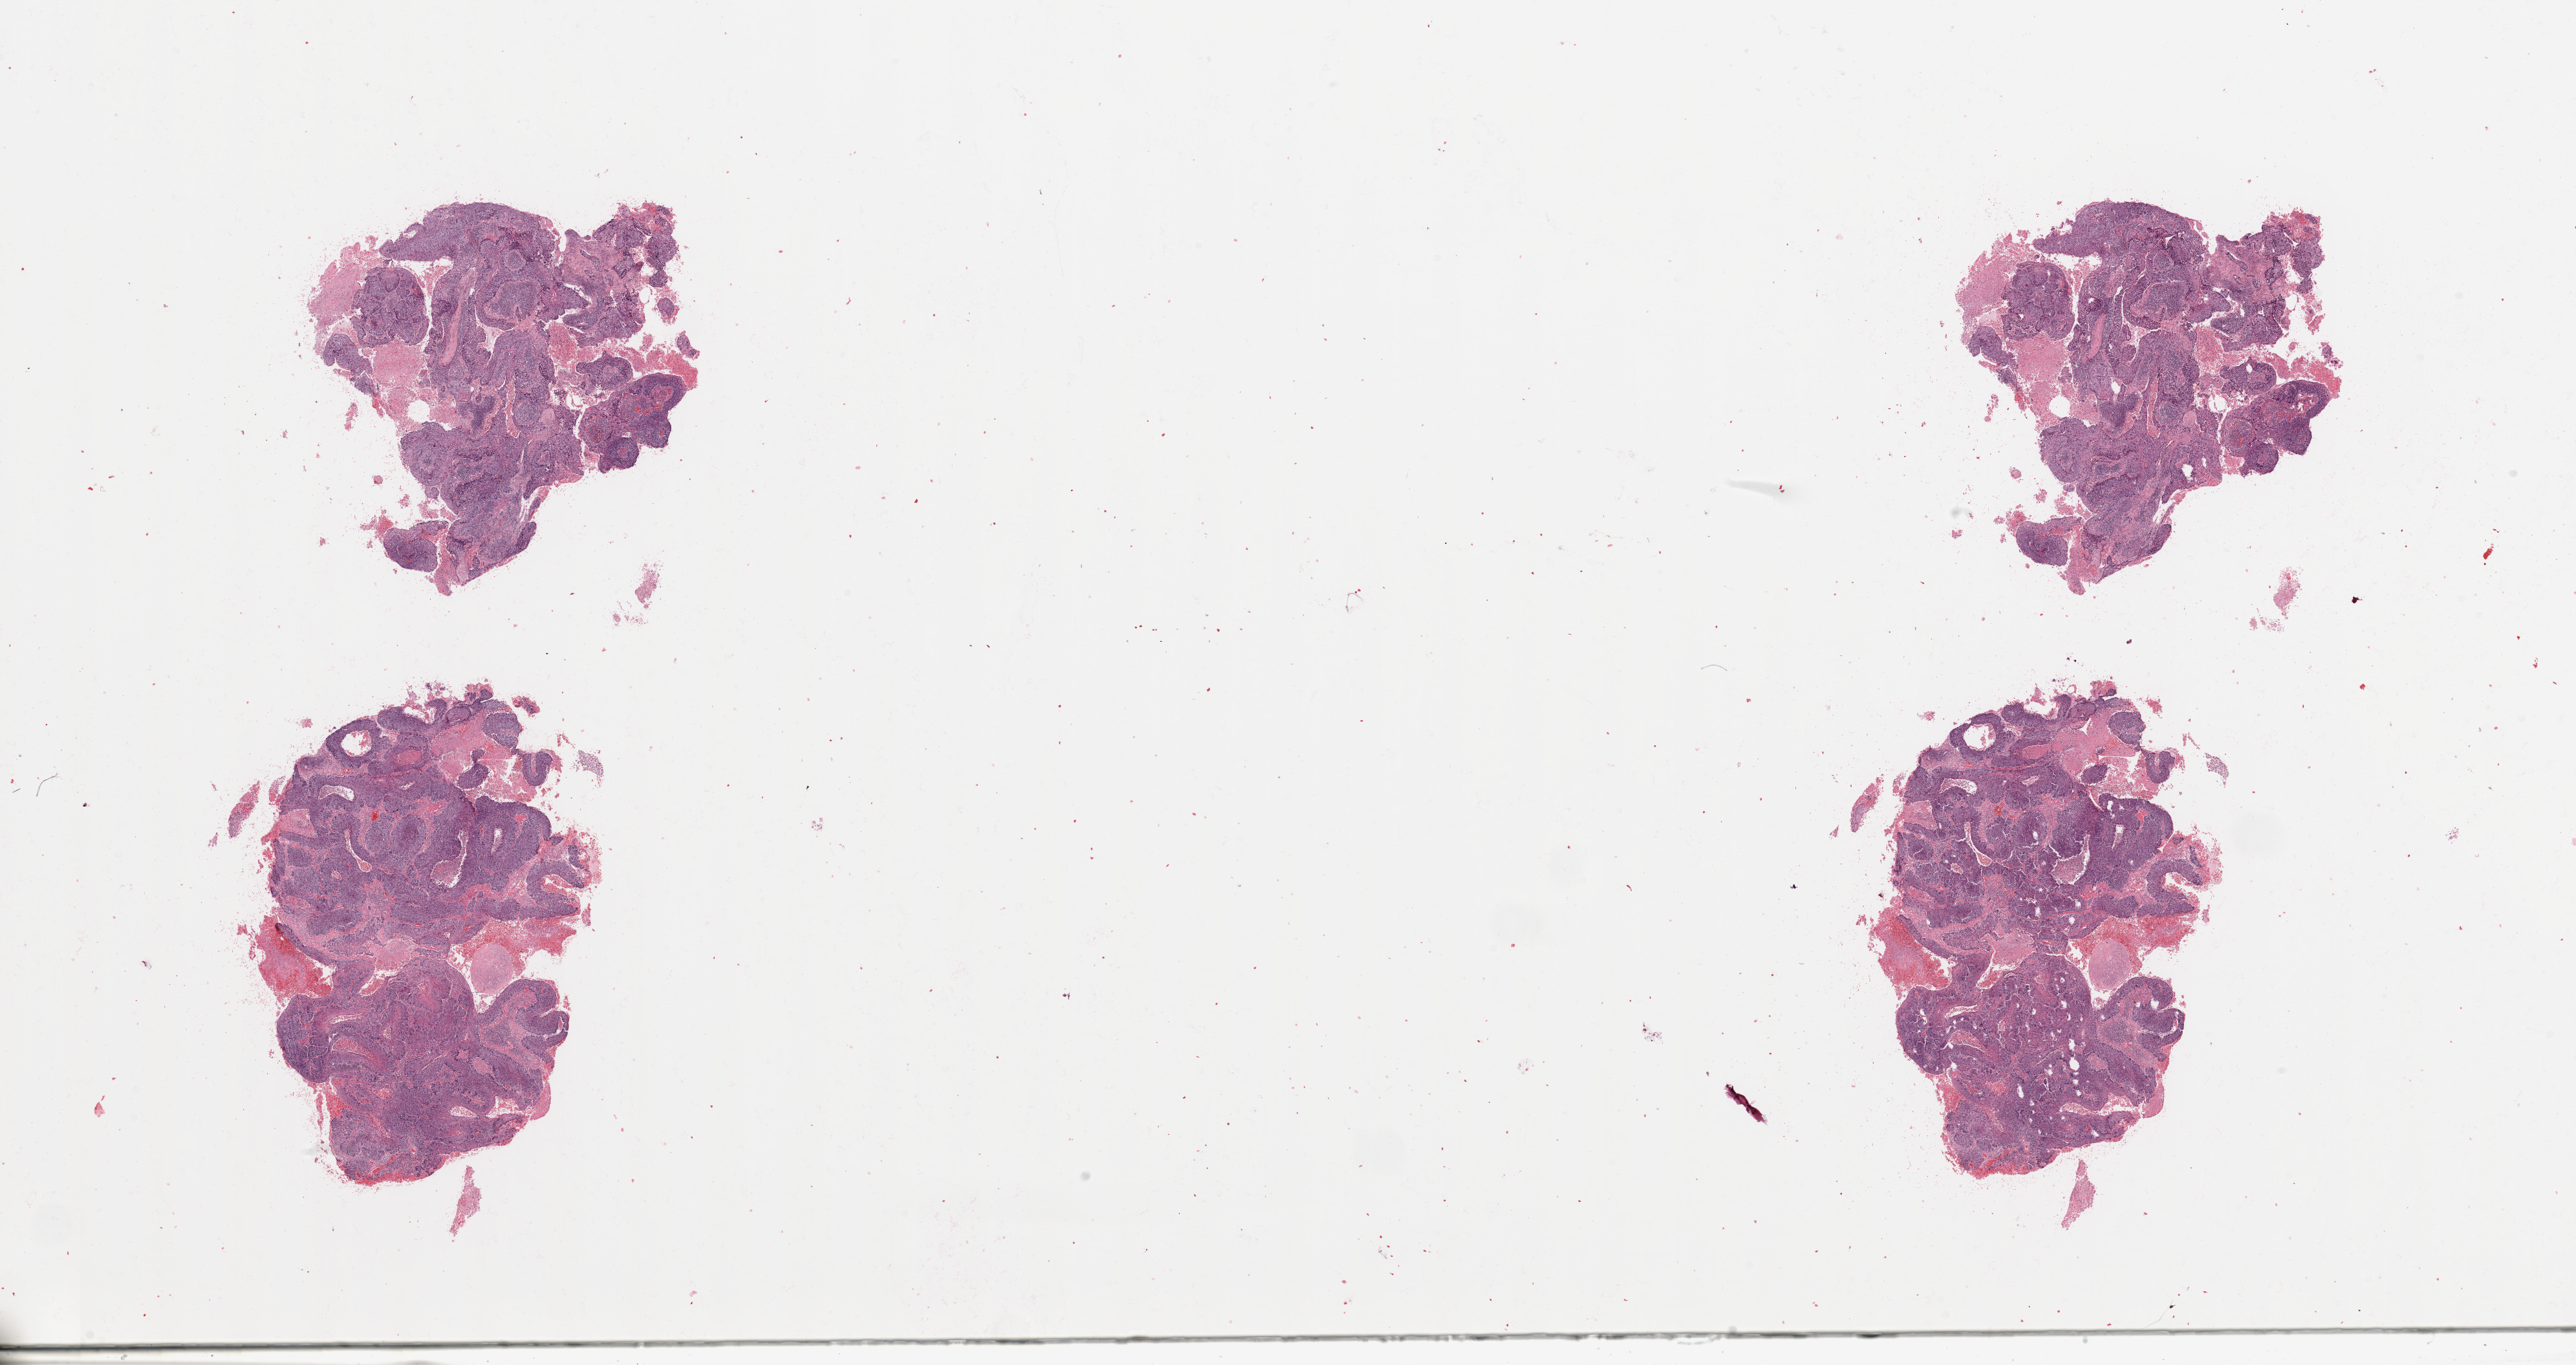
Digitized H&E tissue section (whole slide) — whole scanned area (about 31.5 x 16.7 mm, slide scanned at 20x) shown as a low-resolution overview, tumour tissue sample, sampled site: lung. Male, 74 y/o. Histologic grade: G2 (moderately differentiated). Pathologist review of this section (percent, as recorded): tumour nuclei 85%, necrosis 15%.
* AJCC pathologic stage: IB
* primary tumour site (as recorded): right upper lobe
* histologic diagnosis: Squamous cell carcinoma, NOS